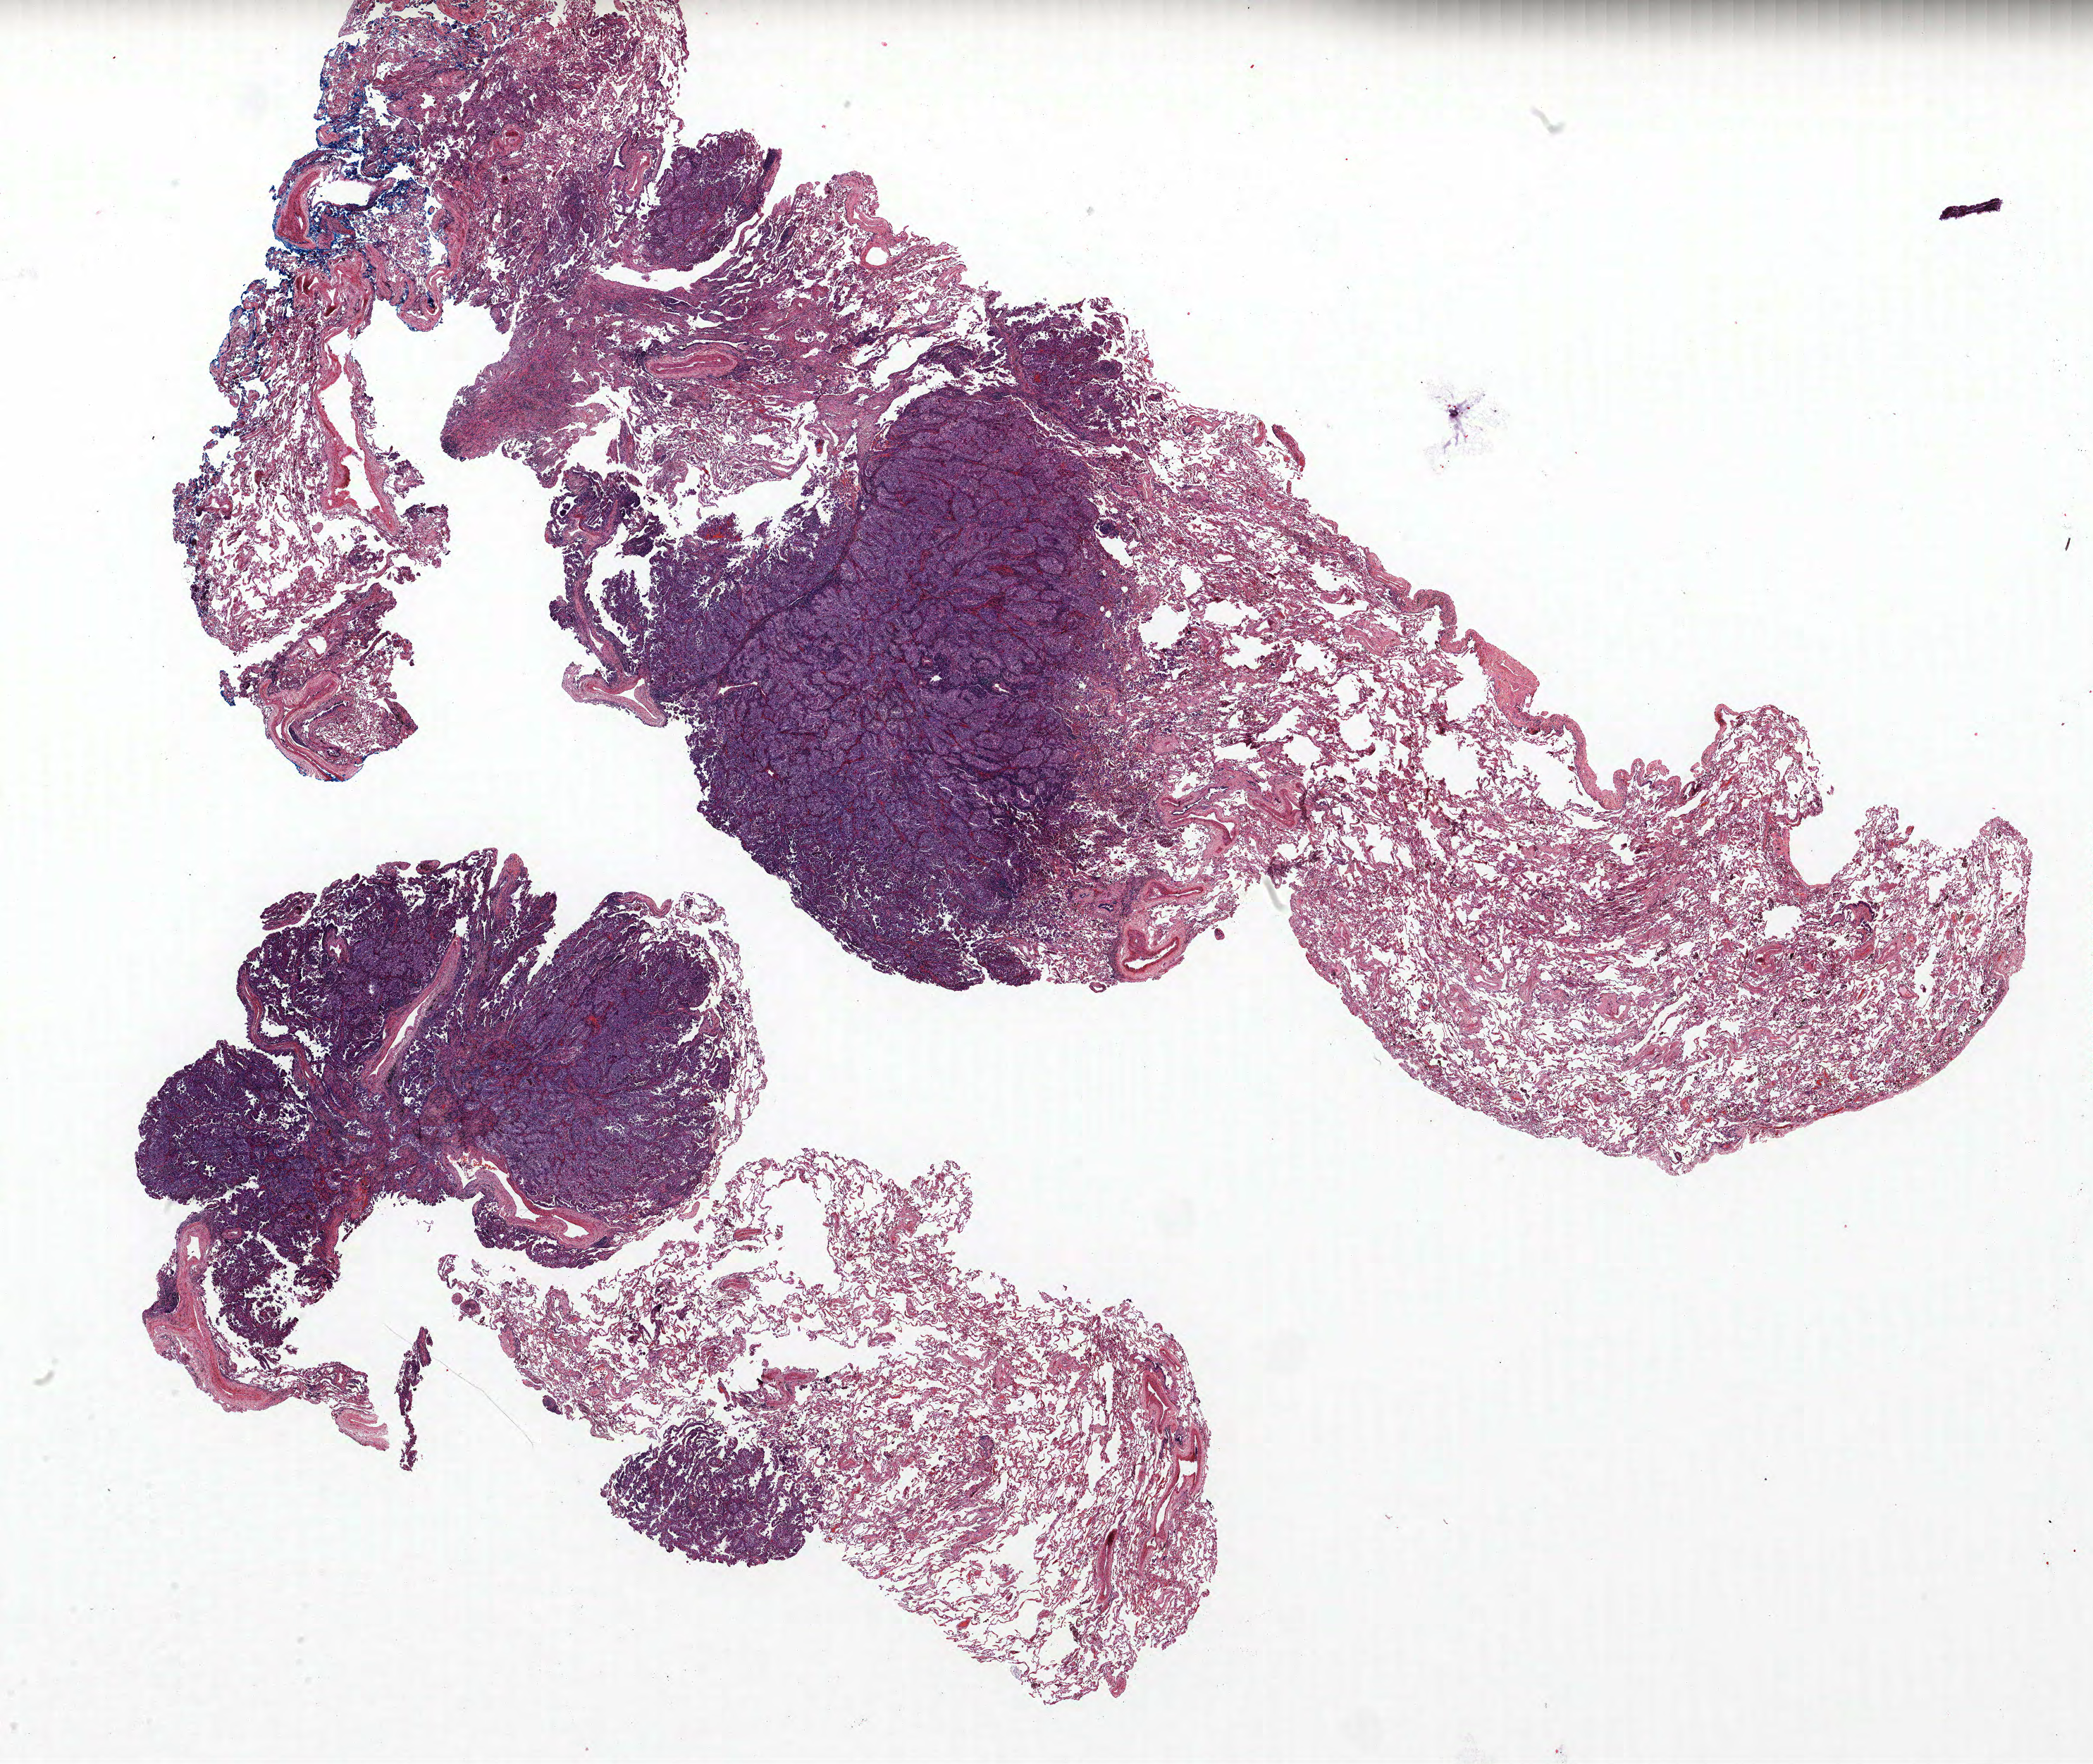
H&E-stained whole-slide image, whole scanned area (about 23.8 x 20.0 mm) shown as a low-resolution overview; FFPE section; lung tissue. Female patient, aged 58 at enrolment. Current smoker at enrolment. Grade: moderately differentiated (G2).
- primary tumour location (clinical record): left lower lobe
- participant's lung-cancer diagnosis: Adenocarcinoma, NOS (ICD-O-3 8140/3)
- stage (AJCC 6th edition): IIIB
- tumour size (pathology): 14 mm
- ICD-O-3 topography: lower lobe of lung (C34.3)